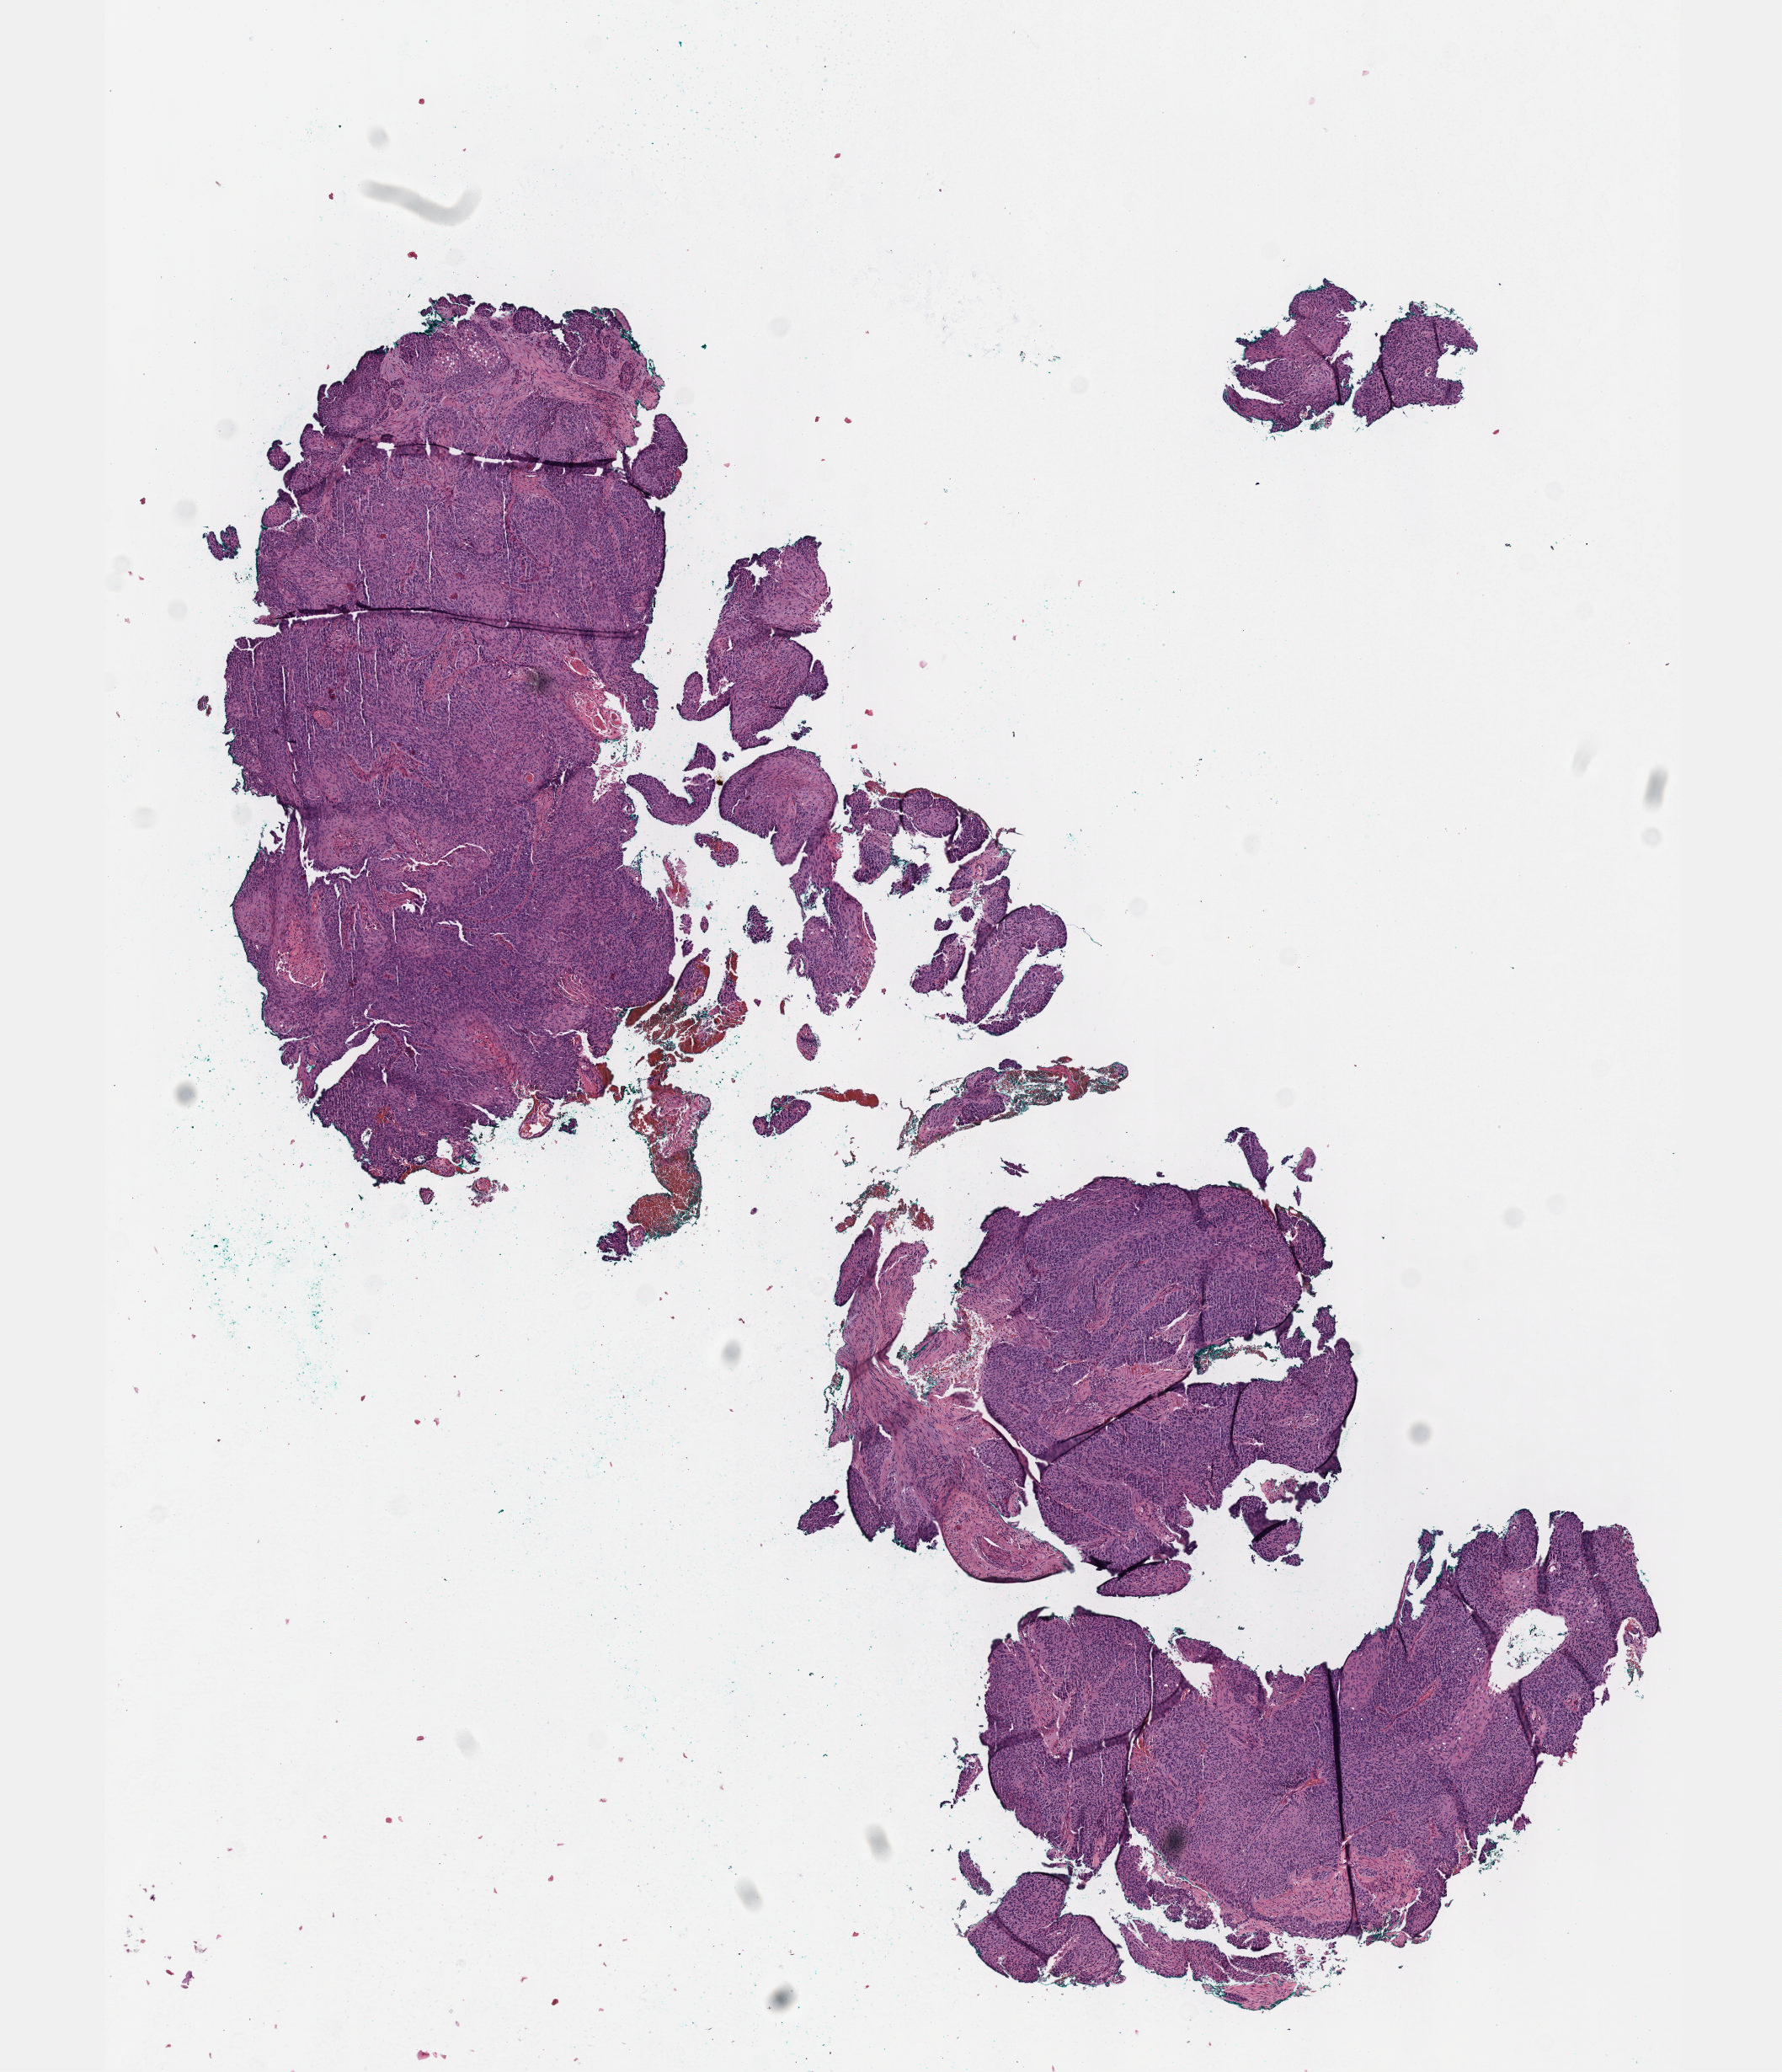
Whole-slide histology image, H&E — shown as a low-resolution overview of the whole scanned area (about 8.6 x 9.9 mm). FFPE section. Cervix, primary tumour sample. Female, age 56 years at initial diagnosis.
Diagnosis: Squamous cell carcinoma, NOS (cervix uteri).